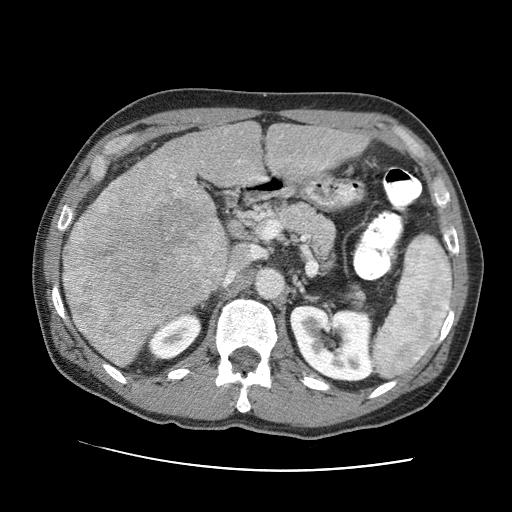
Contrast-enhanced abdominal CT (liver protocol), one axial slice. Slice 42 of 95 in the series (ordered by position). 120 kVp. One of 2 acquisitions stored at this slice position. Soft-tissue window (W 400 / L 40 HU). 2.5 mm slice thickness. 512 × 512 image matrix. Case-level facts recorded for this patient, not image findings: diagnosis: hepatocellular carcinoma (patient treated with transarterial chemoembolisation; whether this scan precedes or follows treatment is not stated here); TNM stage (as recorded): Stage-IVA; Child-Pugh class: A; tumour nodularity: multinodular.
Outlined on this slice (semi-automatic segmentation, software-assisted and operator-edited):
- liver parenchyma outside the tumour (the mass and vessels are separate outlines, so this box may not span the whole liver): bounding box <90,122,368,366> (left, top, right, bottom; pixels)
- mass: <63,176,230,365>
- liver vessels: <139,136,329,181>